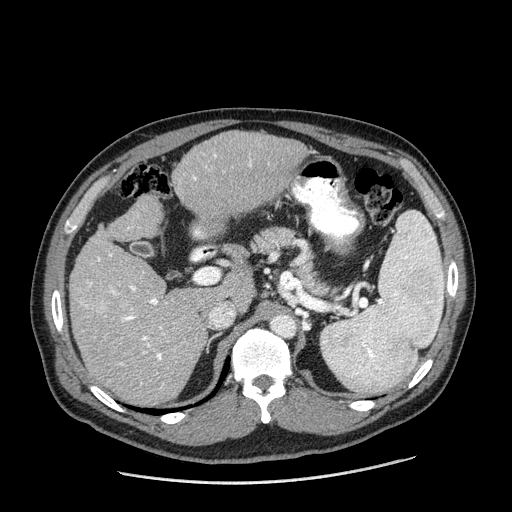
Contrast-enhanced abdominal CT (liver protocol), one axial slice. Slice 109 of 198 in the series (ordered by position). Reconstruction kernel STANDARD. One of 2 acquisitions stored at this slice position. Soft-tissue window (W 400 / L 40 HU). 2.5 mm slice thickness. 512 × 512 image matrix, field of view 400 × 400 mm. Case-level facts recorded for this patient, not image findings: diagnosis: hepatocellular carcinoma (patient treated with transarterial chemoembolisation; whether this scan precedes or follows treatment is not stated here); TNM stage (as recorded): Stage-II; Child-Pugh class: A; tumour differentiation: moderately differentiated; tumour nodularity: multinodular.
Annotated regions visible in this slice (semi-automatically segmented with operator editing):
- liver parenchyma outside the tumour (the mass and vessels are separate outlines, so this box may not span the whole liver): bounding box (x1, y1, x2, y2) in pixels: (68, 130, 306, 404)
- mass: (97, 298, 113, 314)
- liver vessels: (85, 154, 252, 365)